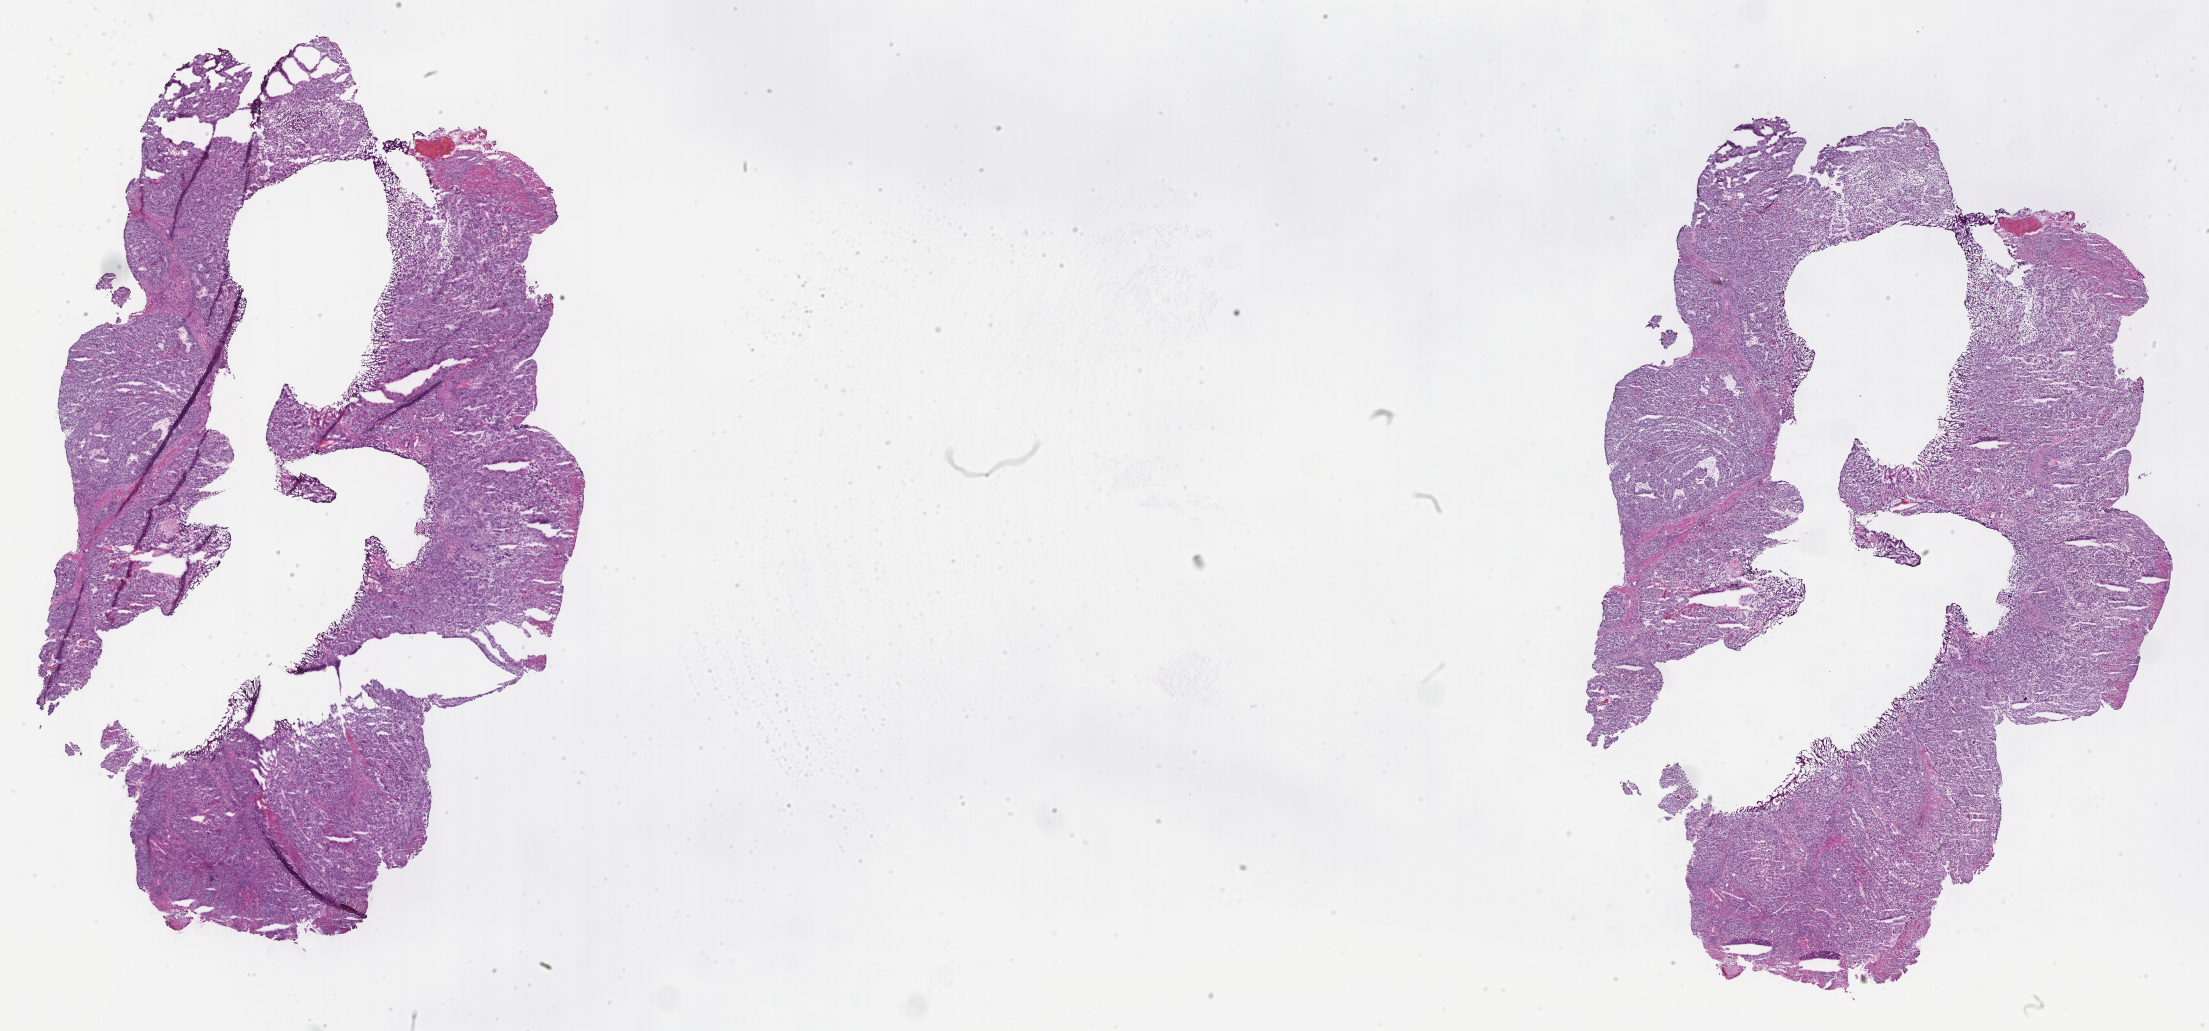
Whole-slide image, H&E stain — whole scanned area (about 35.7 x 16.6 mm) shown as a low-resolution overview; frozen section (tissue freezing medium); specimen: primary tumor. Patient: female, age at initial diagnosis 75 years. Tumor grade: G3 (poorly differentiated). Pathologist review of this section (percent, as recorded): tumor cells 70%, tumor nuclei 80%, stromal cells 5%, necrosis 10%, normal cells 15%. Inflammatory infiltration, as recorded: lymphocyte infiltration 10%, monocyte infiltration 2%, neutrophil infiltration 2%.
Section: top of the tissue portion. Histologic diagnosis: Adenocarcinoma, NOS. AJCC pathologic stage: Stage IIB.